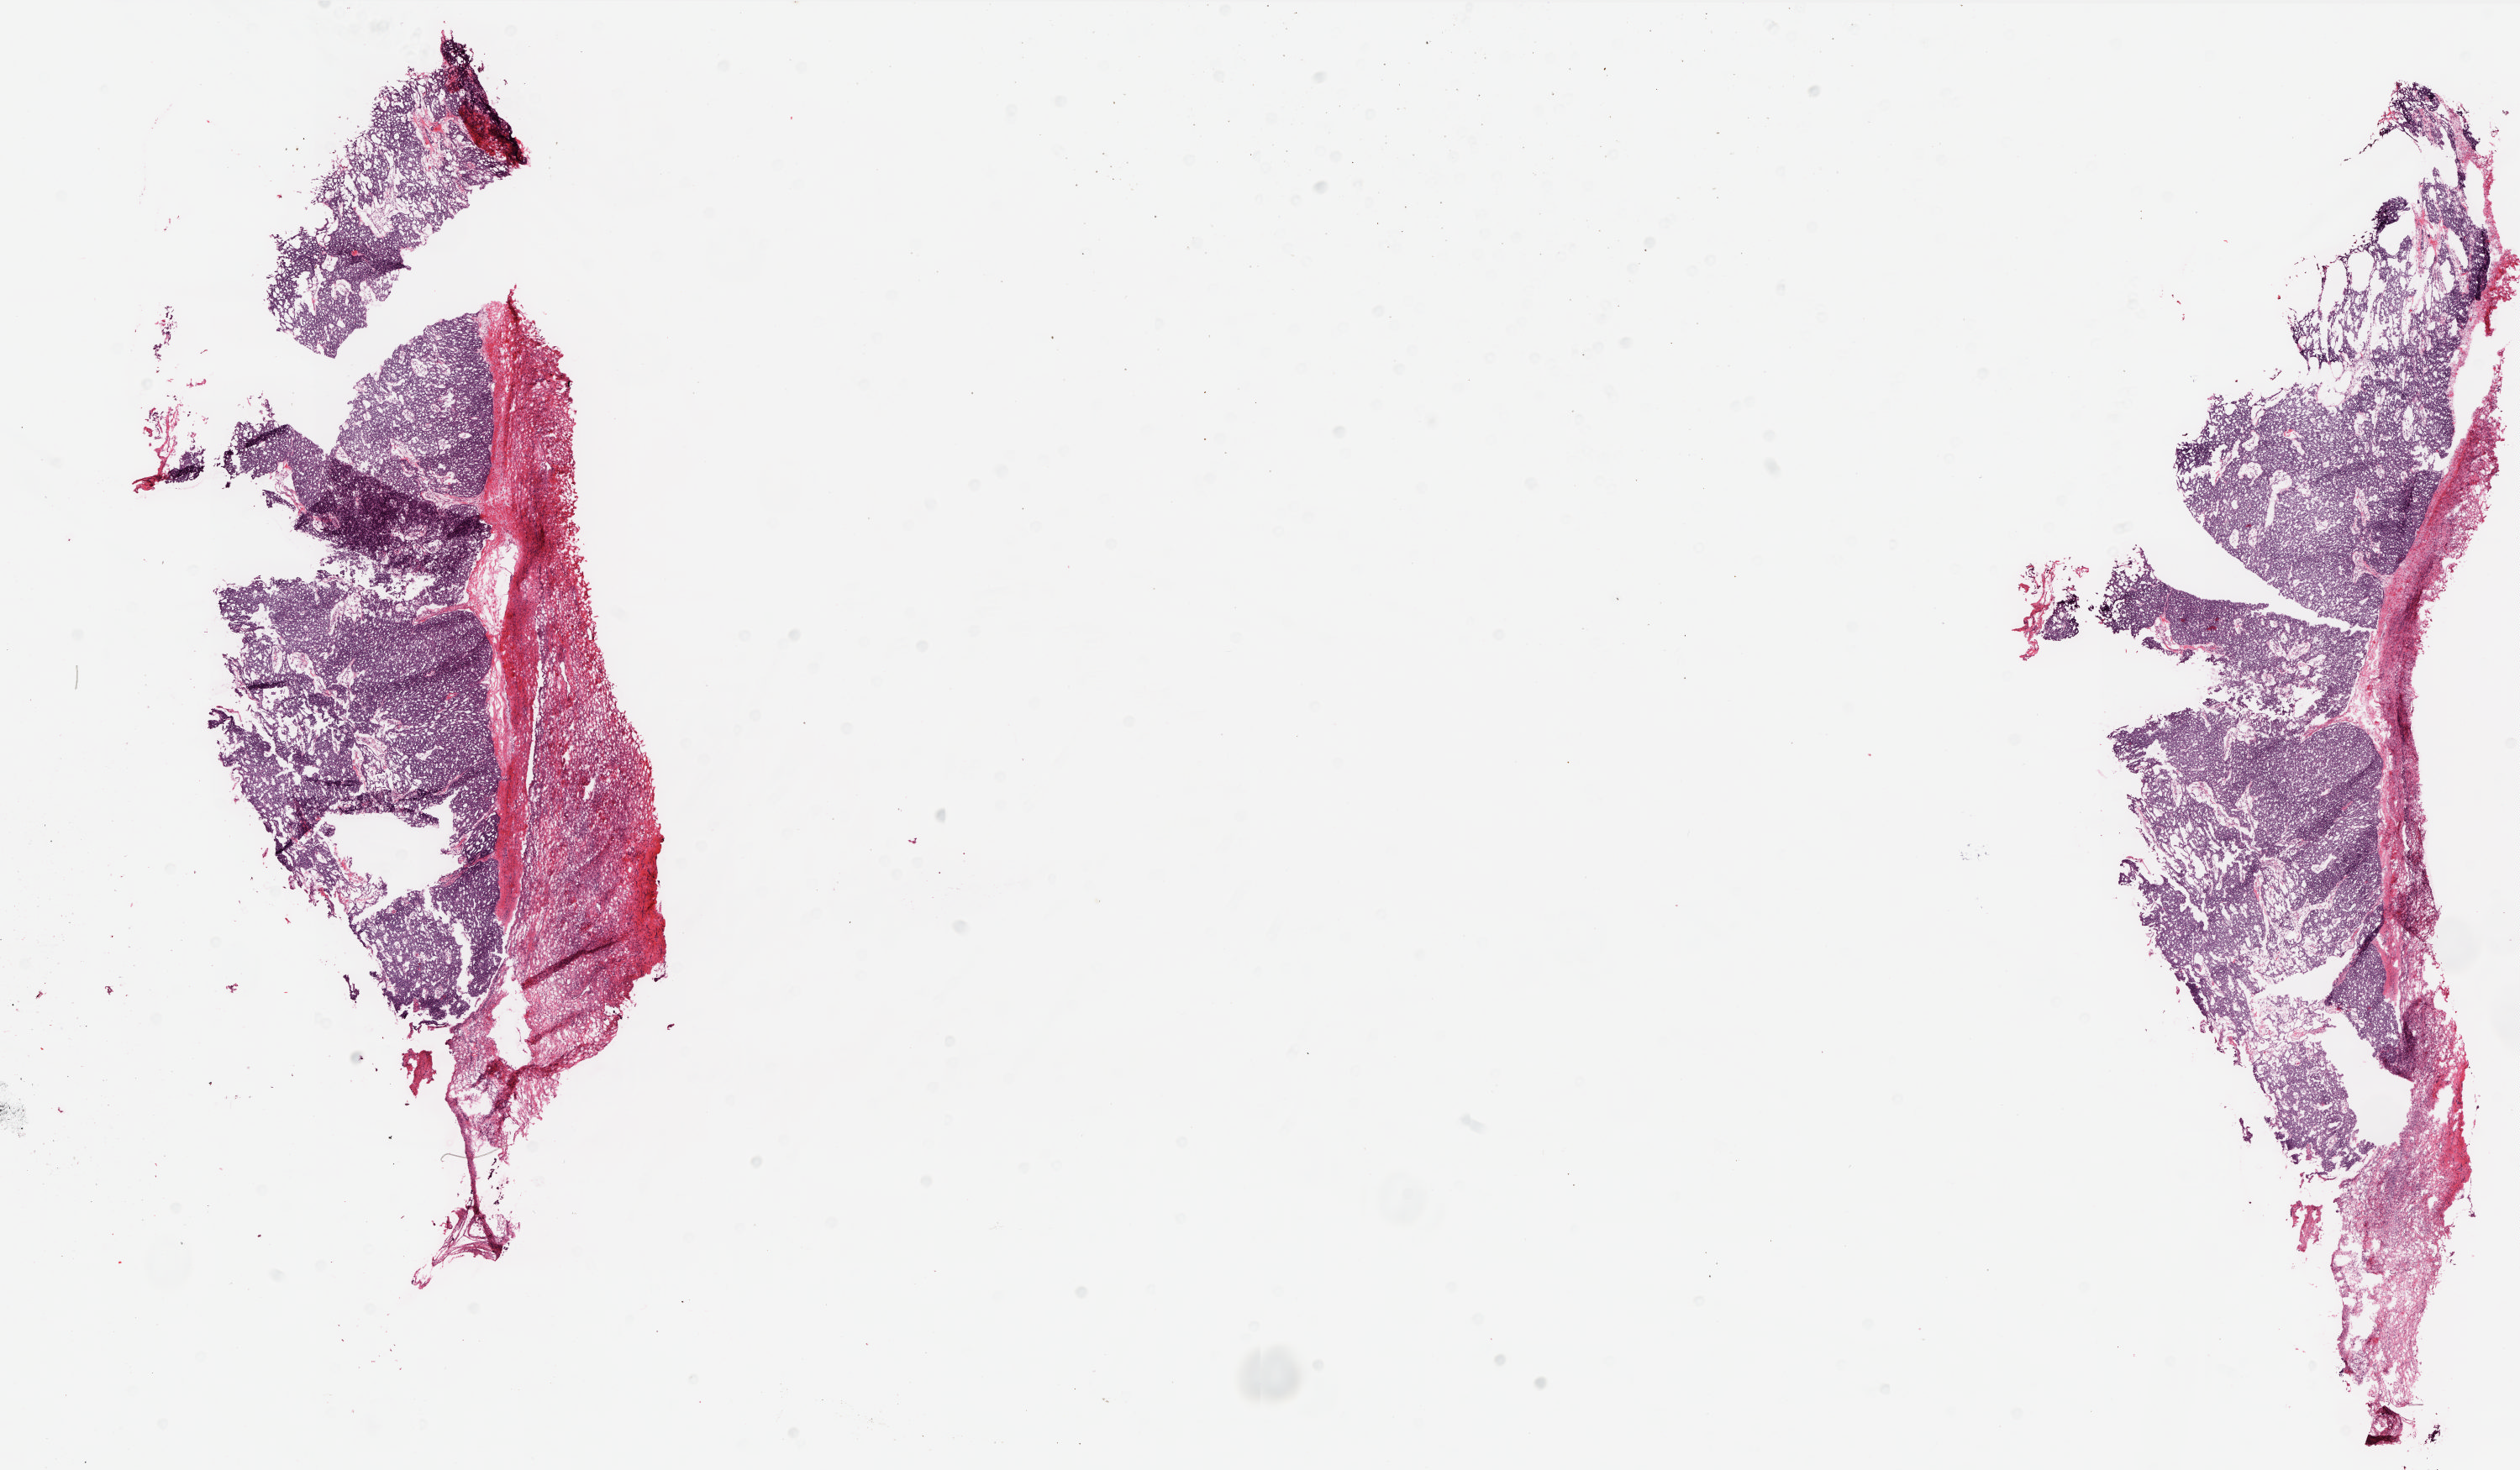
Digitized H&E tissue section (whole slide) — shown as a low-resolution overview of the whole scanned area (about 24.0 x 14.0 mm, acquisition: 20x scan). Frozen section from the top of the tissue portion. Ovary, primary tumour sample. Patient: female, age at initial diagnosis 48 years. Histologic grade: G3 (poorly differentiated). Slide review estimates, as recorded: tumour cells 90%, tumour nuclei 95%, normal cells 0%, stromal cells 10%, necrosis 0%.
Histologic diagnosis: Serous cystadenocarcinoma, NOS. FIGO stage: IIIC.